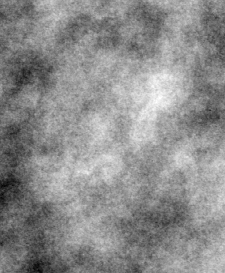
Cropped region of a digitized screen-film mammogram centred on a radiologist-marked abnormality, right breast, MLO view, BI-RADS breast density category 3 (scale 1–4).
- Marked abnormality: calcifications, morphology punctate / pleomorphic, distribution clustered; BI-RADS assessment category 3; pathology result (as recorded, not read from the image): malignant.